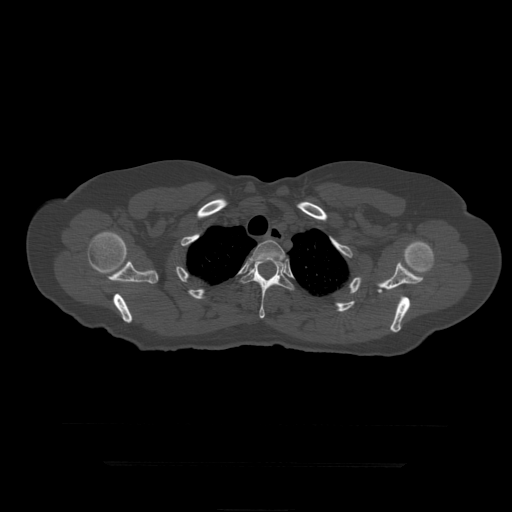
CT including the spine, one axial slice. Slice 354 of 399 in the series (ordered by position). 120 kVp. Bone window (W 1800 / L 400 HU). 1.25 mm slice thickness. 512 × 512 image matrix, field of view 450 × 450 mm. Patient age 41 years. Case-level facts recorded for this patient, not image findings: primary cancer: breast.
Annotated regions visible in this slice (semi-automatically segmented with operator editing):
- T3 vertebra: bounding box (x1, y1, x2, y2) in pixels: (251, 240, 286, 262)
- T4 vertebra: (240, 259, 295, 319)